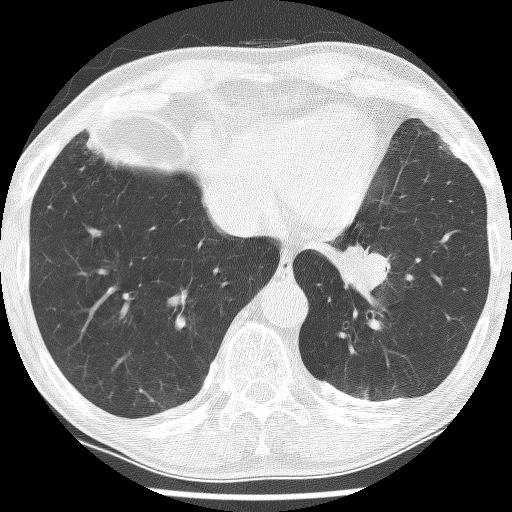
Low-dose screening chest CT, one axial slice. Slice 46 of 226 in the series (ordered by position). Lung window (W 1500 / L -600 HU). 2.5 mm slice thickness. 512 × 512 image matrix, field of view 320 × 320 mm.
Annotated regions visible in this slice (expert manual segmentation):
- lesion 1 (tumor, lower lobe of left lung): bounding box <339,244,391,298> (left, top, right, bottom; pixels)